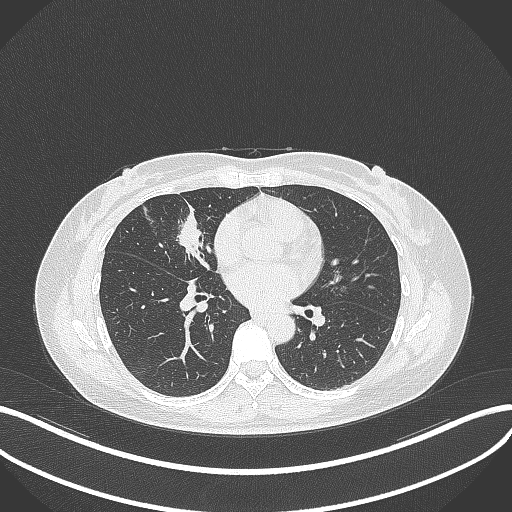
Chest CT, one axial slice; slice 140 of 284 in the series (ordered by position); reconstruction kernel B70f; lung window (W 1500 / L -600 HU); 512 × 512 image matrix. Patient: female, 43 years. Case-level facts recorded for this patient, not image findings: clinical TNM (as recorded): T1c N3 M1; histopathological grade: G1.
Annotated regions visible in this slice (rectangle marked by the reading radiologist):
- lung tumour (recorded histology: adenocarcinoma): bounding box <173,207,208,264> (left, top, right, bottom; pixels)